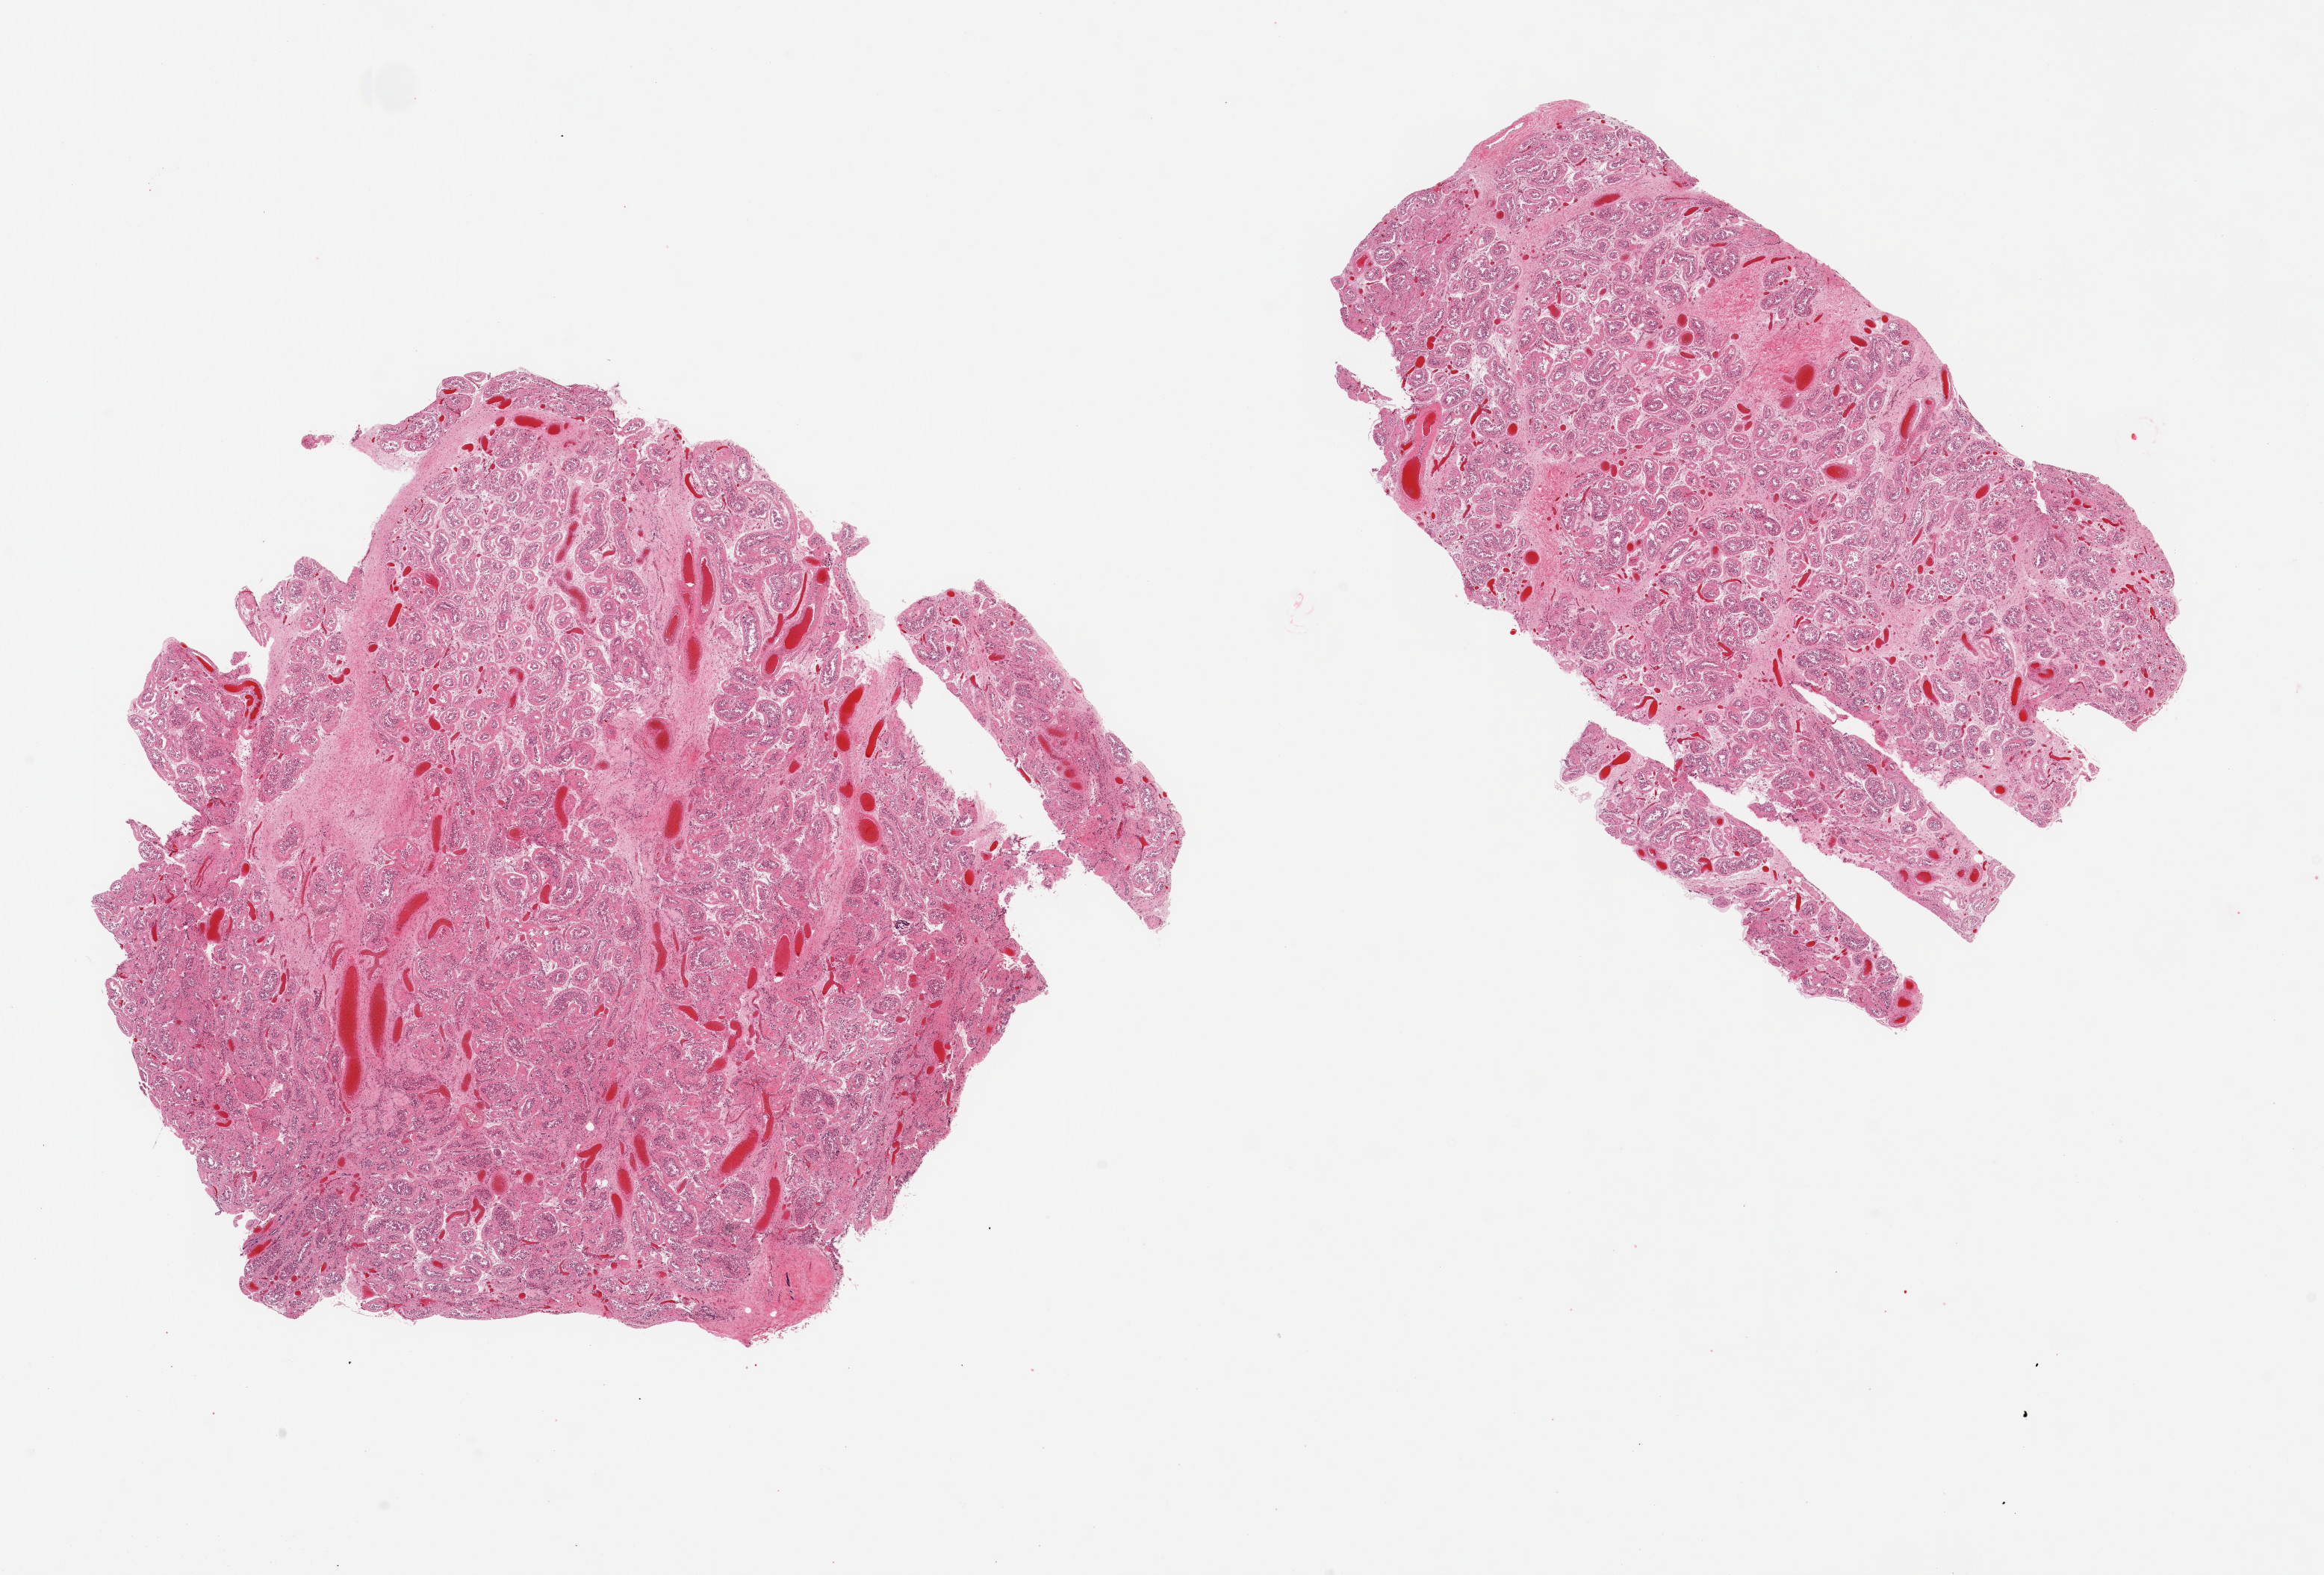
Whole-slide image, haematoxylin and eosin stain, whole scanned area (about 24.6 x 16.7 mm) shown as a low-resolution overview; PAXgene-fixed paraffin-embedded (PFPE) section; section of testis (target tissue); tissue donor sample.
• review note (as recorded): 2 pieces; markedly reduced spermatogenesis